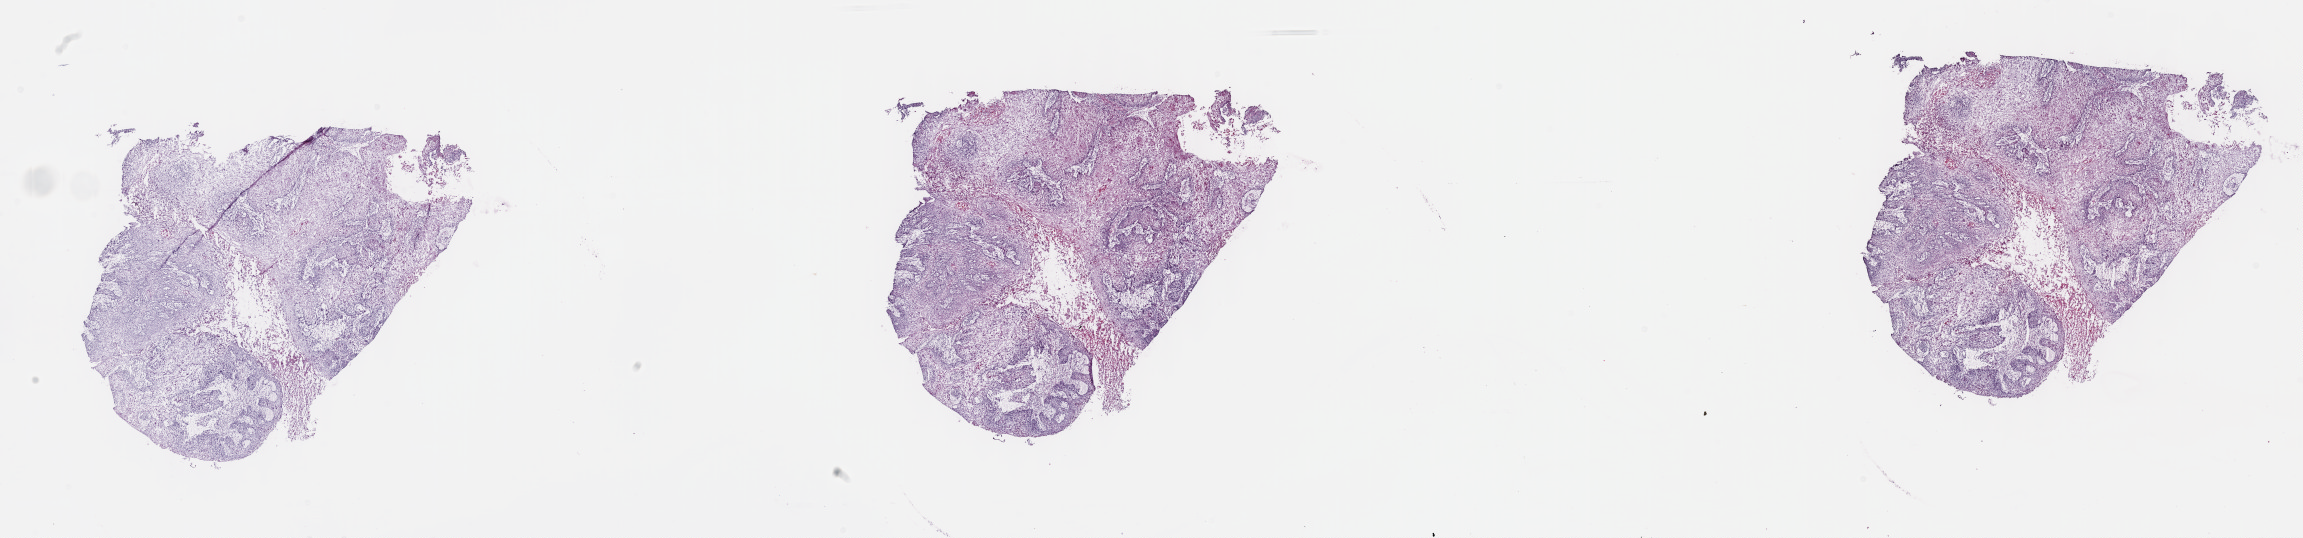
H&E whole-slide image — low-resolution overview of the scanned area, about 37.2 x 8.7 mm (slide scanned at 40x). Frozen section from the top of the tissue portion. Esophagus, primary tumour sample. Male patient; age at initial diagnosis 67 years. Histologic grade: GX (grade cannot be assessed). Pathologist review of this section (percent, as recorded): tumour cells 97%, tumour nuclei 80%, normal cells 0%, stromal cells 0%, necrosis 3%. Inflammatory infiltration, as recorded: lymphocyte infiltration 4%, monocyte infiltration 0%, neutrophil infiltration 1%.
TNM: T3 N0 MX. AJCC pathologic stage: IIA (6th edition). Histologic diagnosis: Squamous cell carcinoma, NOS (lower third of esophagus).